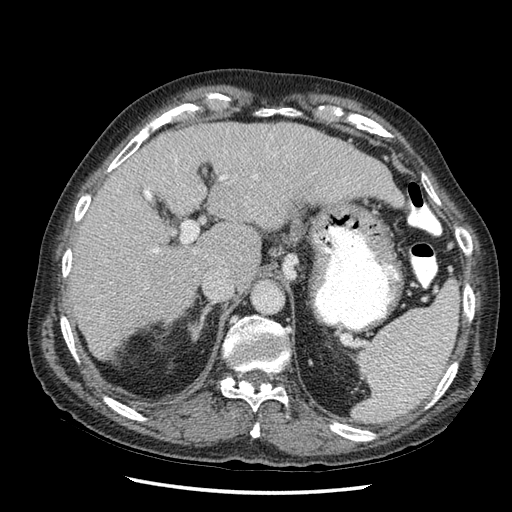
Contrast-enhanced abdominal CT (liver protocol), one axial slice. Reconstruction kernel STANDARD. 120 kVp. Soft-tissue window (W 400 / L 40 HU). 512 × 512 image matrix, field of view 360 × 360 mm. Case-level facts recorded for this patient, not image findings: diagnosis: hepatocellular carcinoma (patient treated with transarterial chemoembolisation; whether this scan precedes or follows treatment is not stated here); TNM stage (as recorded): Stage-I; Child-Pugh class: A; tumour nodularity: uninodular.
Outlined on this slice (semi-automatically segmented with operator editing):
- liver parenchyma outside the tumour (the mass and vessels are separate outlines, so this box may not span the whole liver): box from (x=64, y=120) to (x=402, y=370) px
- liver vessels: (x=120, y=146)–(x=221, y=276)